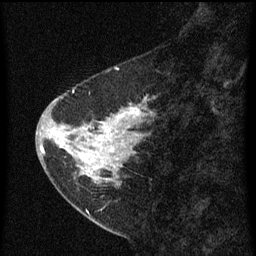
Breast MRI (dynamic contrast-enhanced), one sagittal slice. Position 21 of 60 along the scan axis. Dynamic contrast-enhanced series, image 2 of 3 at this slice position (ordered by acquisition). 1.5 T. TE 4.2 ms, TR 8 ms. 2 mm slice thickness. 256 × 256 image matrix. Female patient, age 47 years.
Structures marked on this image (semi-automatic segmentation, software-assisted and operator-edited):
- analysis volume of interest (the breast-tissue region the enhancement analysis was run in; not a lesion): bounding box (x1, y1, x2, y2) in pixels: (44, 84, 153, 199)
- tumour enhancement mask (voxels above the 70 % enhancement threshold inside the analysis volume of interest): (44, 90, 147, 177)